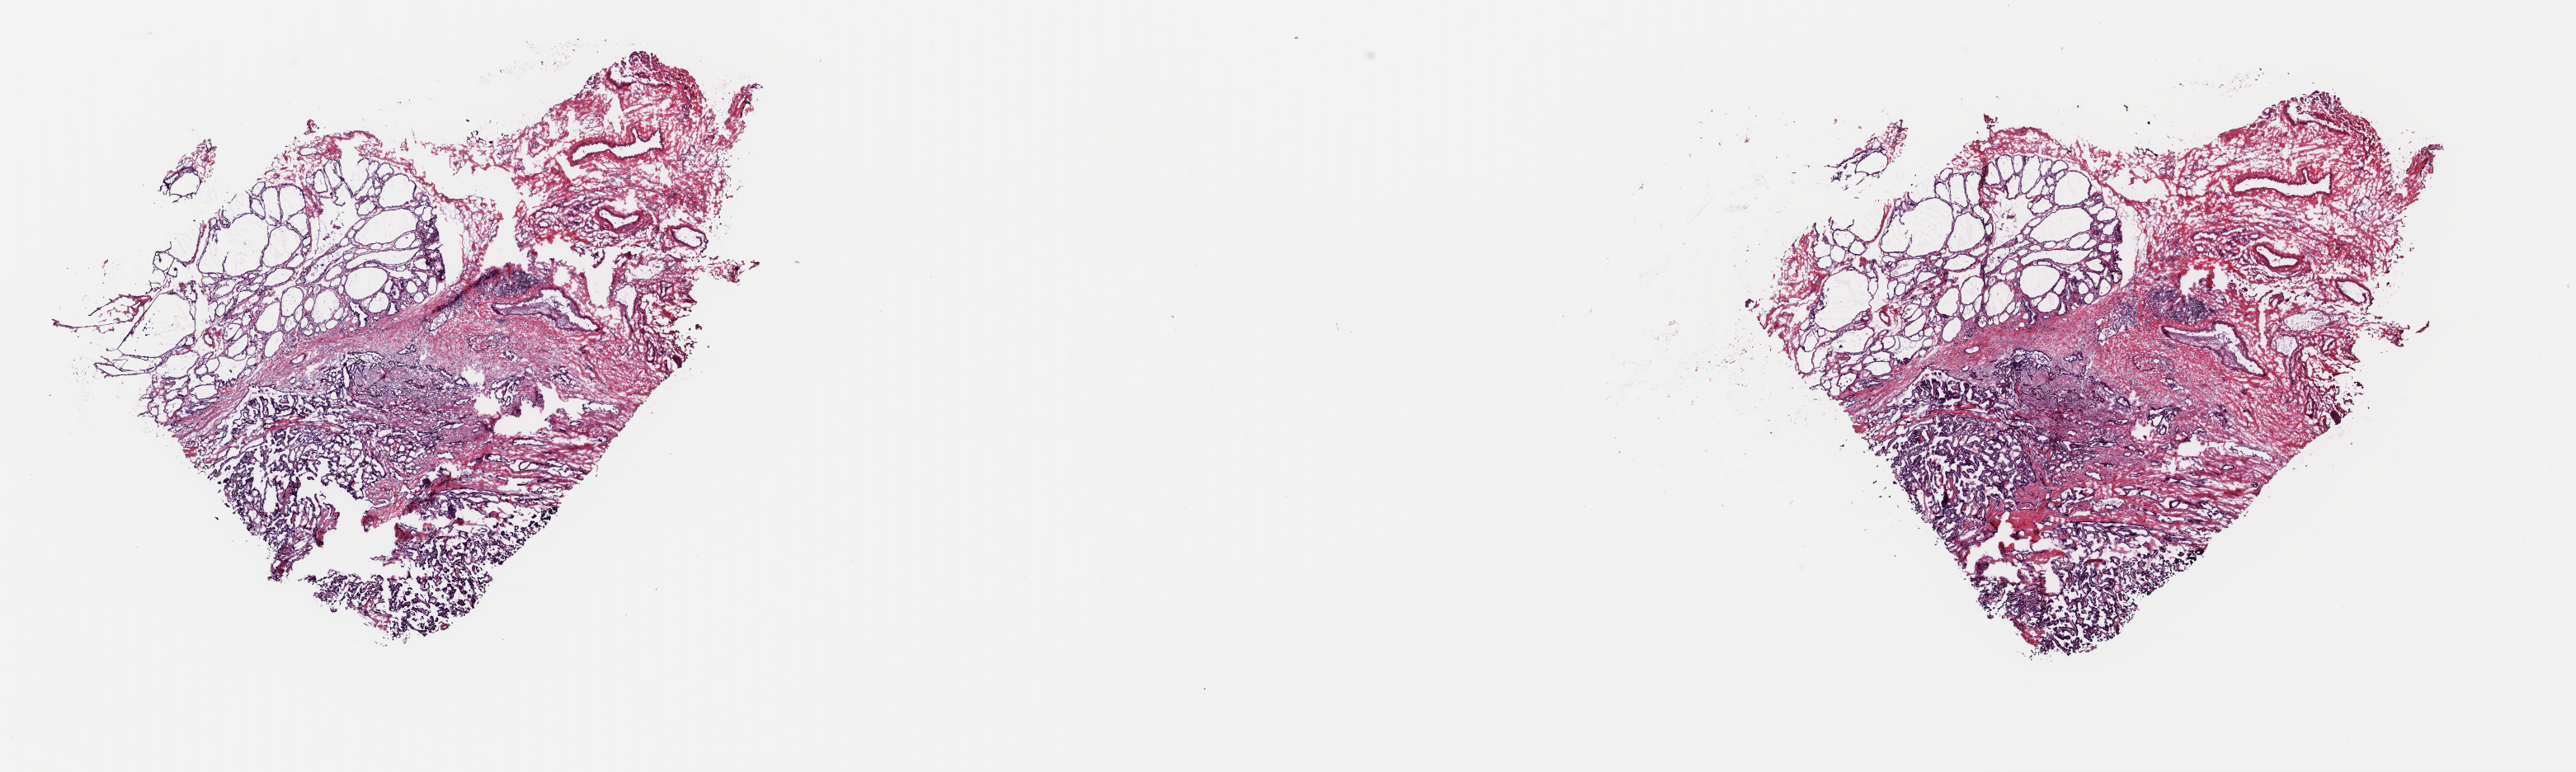
Whole-slide histology image, H&E-stained, a low-resolution overview of the entire scanned area, about 24.7 x 7.4 mm, frozen section from the top of the tissue portion, thyroid, primary tumour sample. Female, age 25 years at initial diagnosis. Composition of this section per pathologist review: tumour cells 70%, tumour nuclei 70%, normal cells 20%, stromal cells 10%, necrosis 0%. Infiltration values recorded for this section: lymphocyte infiltration 10%, monocyte infiltration 0%, neutrophil infiltration 0%.
Lymph nodes positive (case pathology): 0 of 2 examined. Laterality: right. AJCC pathologic stage: I (7th edition). Pathologic diagnosis: Papillary adenocarcinoma, NOS (thyroid gland).